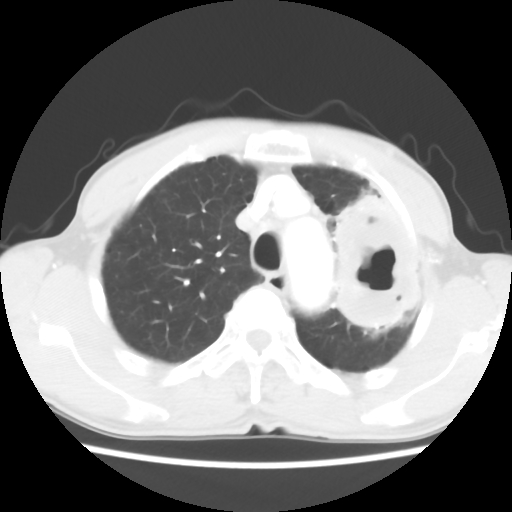
Chest CT, one axial slice. Position 46 of 60 along the scan axis. Reconstruction kernel STANDARD. Lung window (W 1500 / L -600 HU). 5 mm slice thickness. 512 × 512 image matrix, field of view 308 × 308 mm. Male patient, age 64 years. From the clinical record (not read from this slice): clinical TNM (as recorded): T3 N3 M0; histopathological grade: G3.
Structures marked on this image (bounding box drawn by a radiologist):
- lung tumour (recorded histology: adenocarcinoma): bounding box [x1, y1, x2, y2] px = [310, 179, 428, 347]